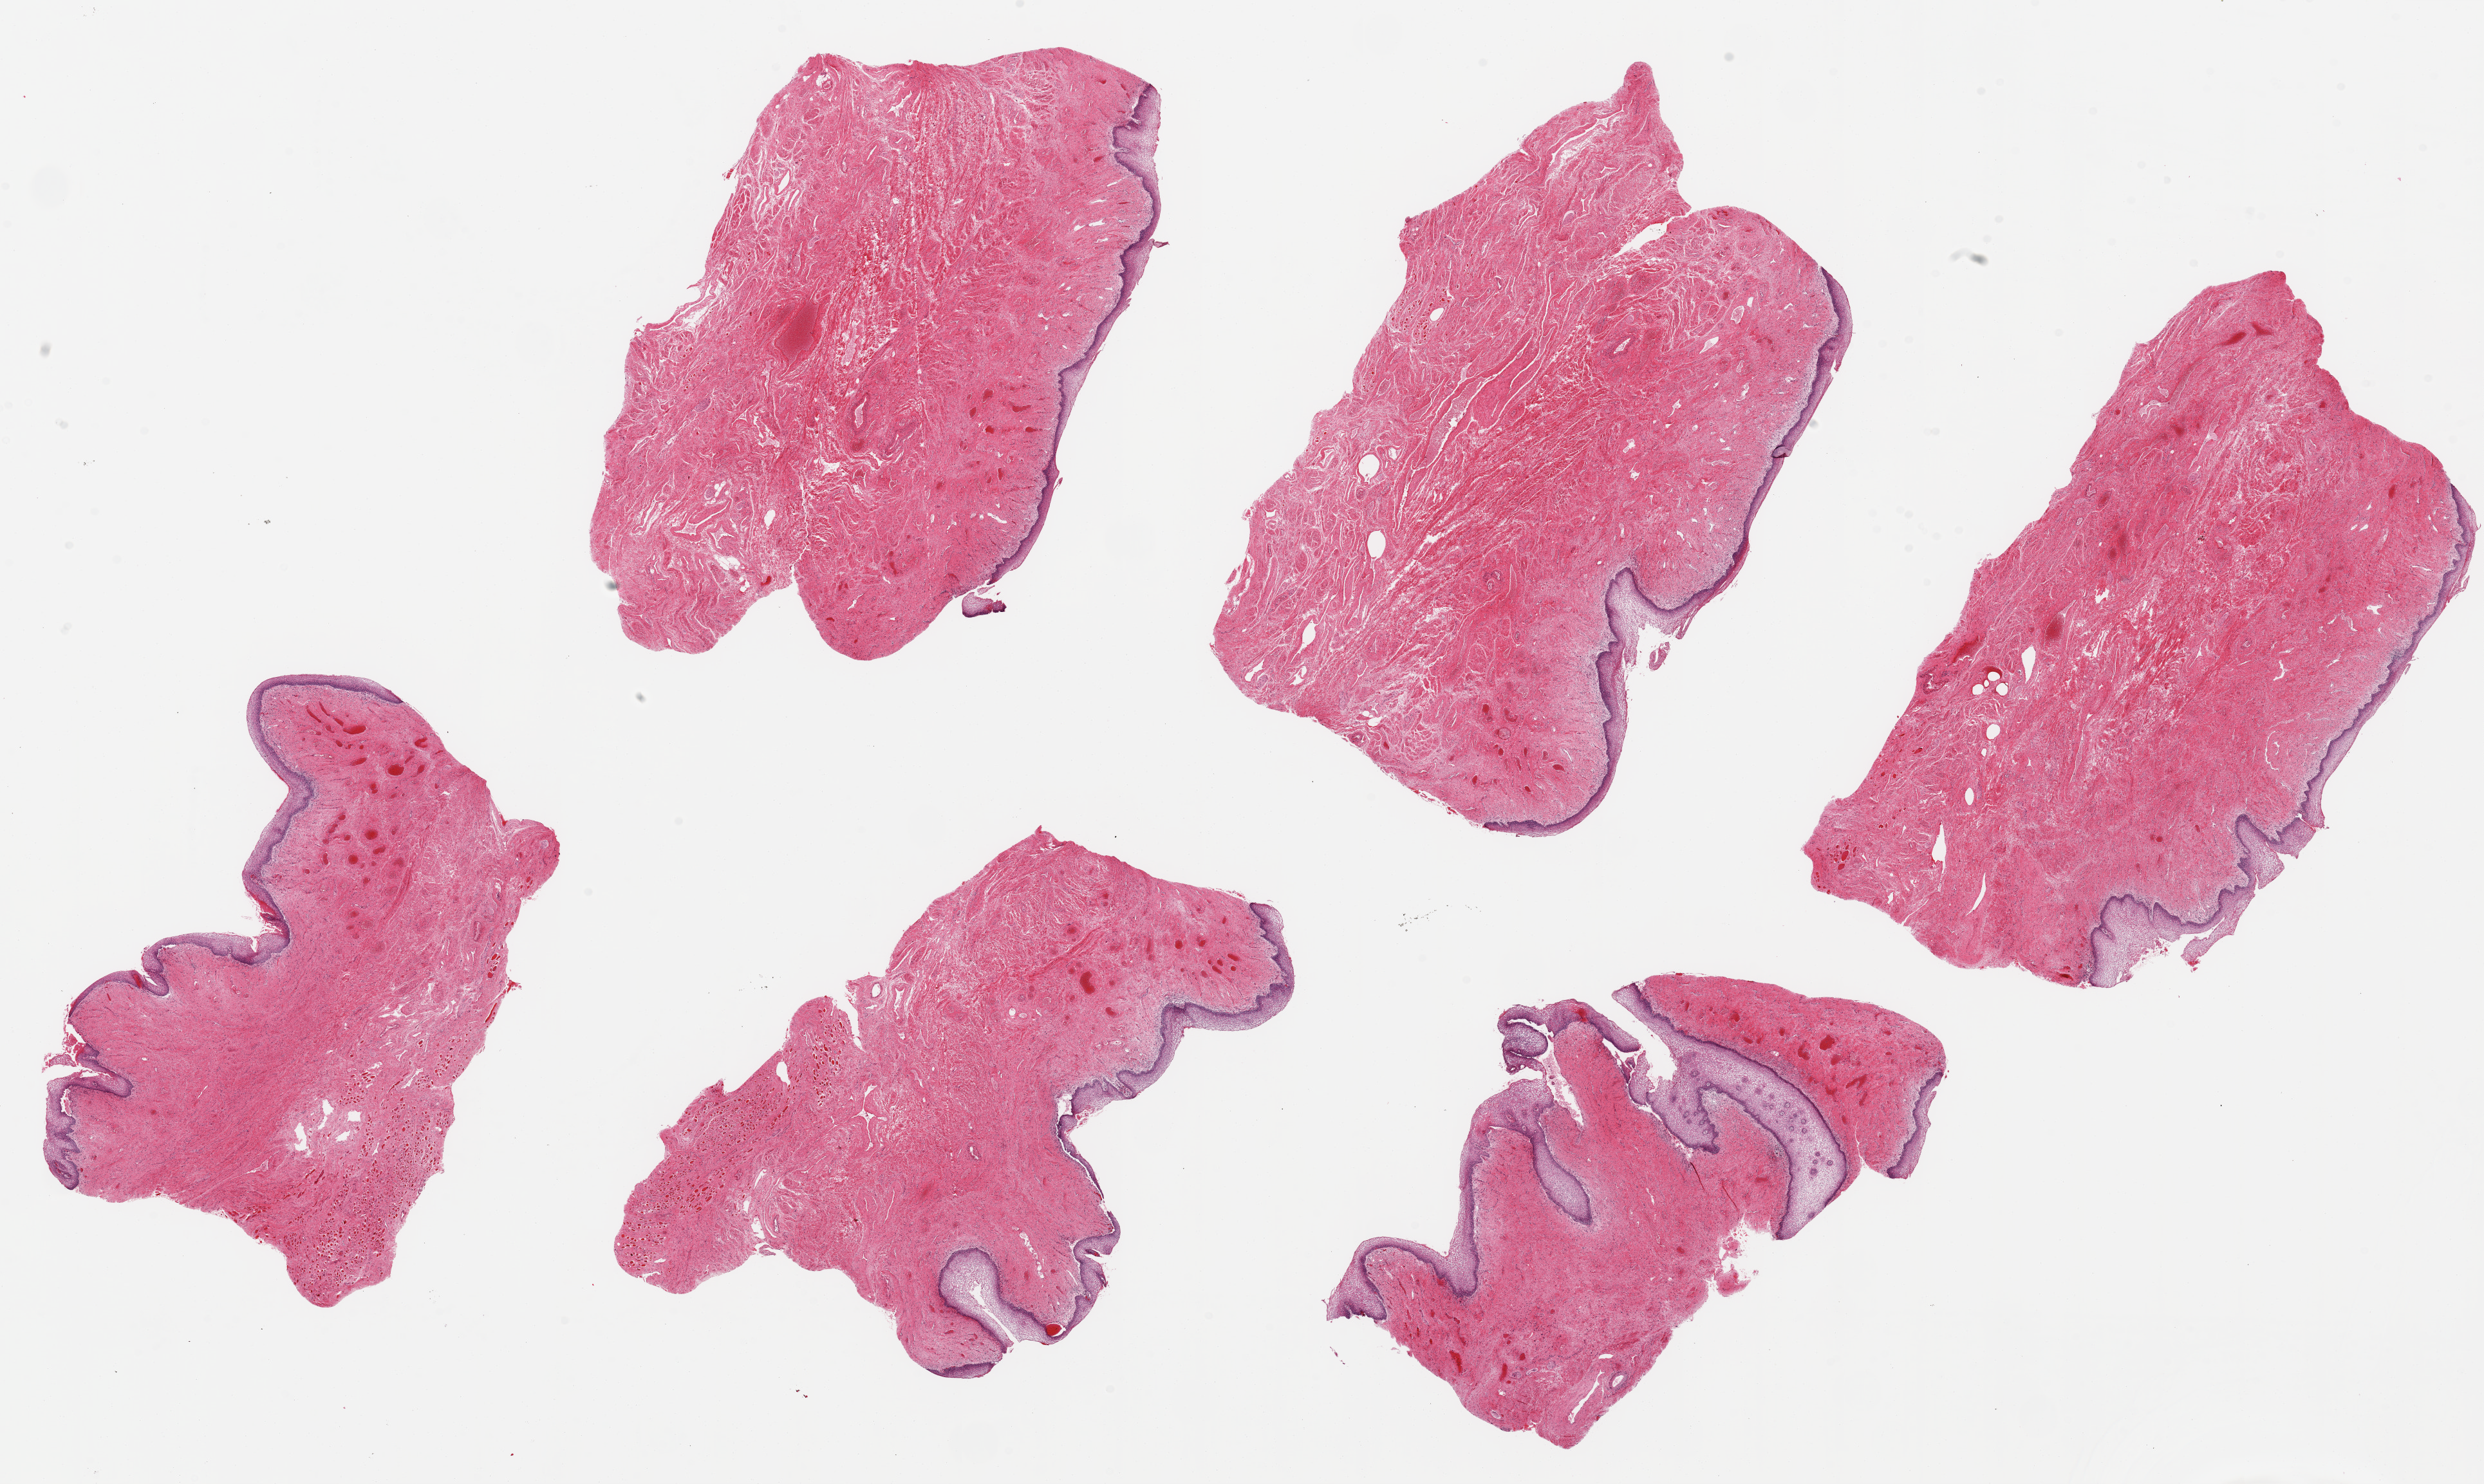
Haematoxylin and eosin whole-slide image — a low-resolution overview of the entire scanned area, about 30.5 x 18.2 mm (acquisition: 20x scan). PAXgene-fixed, paraffin-embedded tissue. Section of vagina (target tissue). Donor tissue sample. Female donor.
Review note (as recorded): 6 ~9x4.5mm pieces. Squamous mucosa is ~3-5% of thickness.